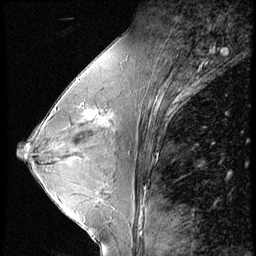
Breast MRI (dynamic contrast-enhanced), one sagittal slice; position 34 of 56 along the scan axis; 4 images stored at this slice position (order not interpretable as contrast timing); 1.5 T; TE 4.2 ms, TR 9 ms; 2.5 mm slice thickness; 256 × 256 image matrix, field of view 180 × 180 mm. Female patient, age 45 years. From the clinical record (not read from this slice): setting: breast cancer imaged before/during neoadjuvant chemotherapy; receptor status: triple-negative.
Annotated regions visible in this slice (semi-automatically segmented with operator editing):
- analysis volume of interest (the breast-tissue region the enhancement analysis was run in; not a lesion): bounding box <77,104,97,124> (left, top, right, bottom; pixels)
- tumour enhancement mask (voxels above the 140 % enhancement threshold inside the analysis volume of interest): <77,104,97,123>